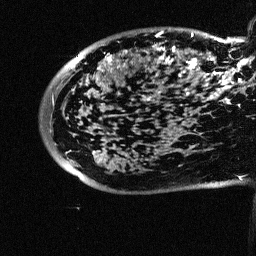
Breast MRI (dynamic contrast-enhanced), one sagittal slice; position 14 of 64 along the scan axis; dynamic contrast-enhanced study with each time point stored as its own series, time point 2 of 3 at this slice position (early post-contrast, ordered by acquisition time); 1.5 T; TE 4.5 ms, TR 11 ms; 256 × 256 image matrix, field of view 200 × 200 mm. Female patient, age 38 years. From the clinical record (not read from this slice): setting: breast cancer imaged before/during neoadjuvant chemotherapy; receptor status: HR-positive, HER2-negative.
Outlined on this slice (semi-automatically segmented with operator editing):
- analysis volume of interest (the breast-tissue region the enhancement analysis was run in; not a lesion): bounding box (x1, y1, x2, y2) in pixels: (88, 18, 252, 126)
- tumour enhancement mask (voxels above the 90 % enhancement threshold inside the analysis volume of interest): (108, 31, 252, 104)